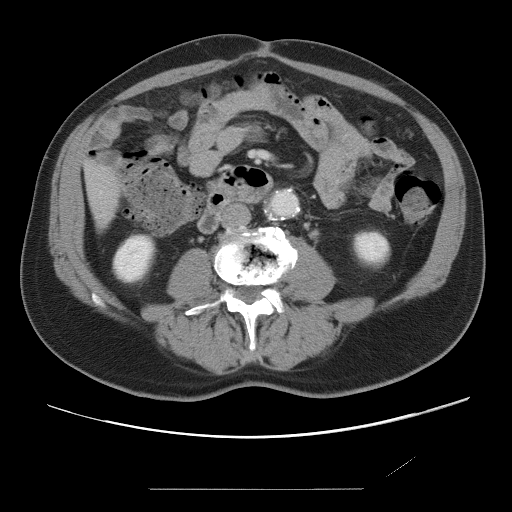
Contrast-enhanced abdominal CT, one axial slice. Slice 10 of 87 in the series (ordered by position). 120 kVp. Intravenous contrast given. Soft-tissue window (W 400 / L 40 HU). 512 × 512 image matrix. Male patient, age 74 years. From the clinical record (not read from this slice): diagnosis: colorectal cancer liver metastases, imaged before liver resection.
Annotated regions visible in this slice (outlined manually by an expert reader):
- liver: box from (x=86, y=164) to (x=118, y=225) px
- planned liver remnant (the part of the liver to remain after resection): (x=86, y=164)–(x=118, y=225)